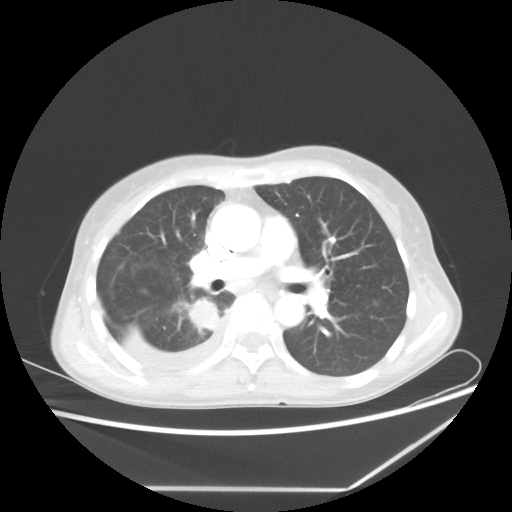
Chest CT, one axial slice. Slice 34 of 60 in the series (ordered by position). Reconstruction kernel STANDARD. Lung window (W 1500 / L -600 HU). 512 × 512 image matrix, field of view 364 × 364 mm. Patient: female, 59 years. Case-level facts recorded for this patient, not image findings: clinical TNM (as recorded): T1c N1 M1.
Structures marked on this image (rectangle marked by the reading radiologist):
- lung tumour (recorded histology: adenocarcinoma): bounding box [x1, y1, x2, y2] px = [180, 292, 221, 333]